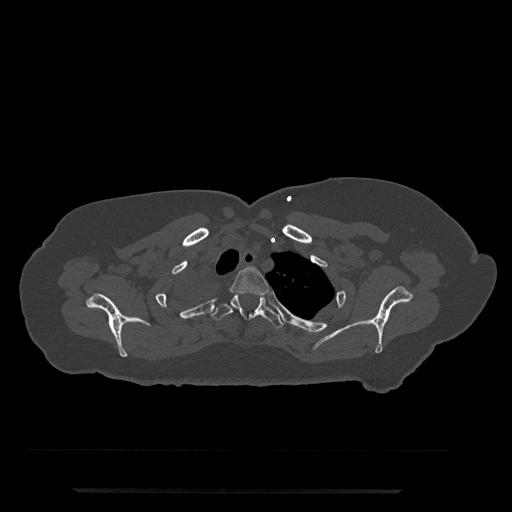
CT including the spine, one axial slice; slice 650 of 797 in the series (ordered by position); reconstruction kernel Br40s/3; bone window (W 1800 / L 400 HU); 512 × 512 image matrix, field of view 440 × 440 mm. Patient: female, 51 years. From the clinical record (not read from this slice): primary cancer: neuro; vertebrae with lytic lesions (as recorded): T8.
Annotated regions visible in this slice (semi-automatic segmentation, software-assisted and operator-edited):
- T2 vertebra: bounding box <229,267,269,296> (left, top, right, bottom; pixels)
- T3 vertebra: <210,293,284,328>